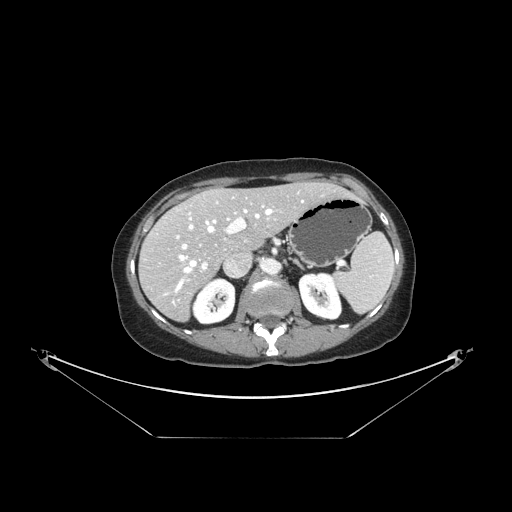
Contrast-enhanced abdominal CT, one axial slice. Slice 91 of 148 in the series (ordered by position). Intravenous contrast given. Soft-tissue window (W 400 / L 40 HU). 2.5 mm slice thickness. 512 × 512 image matrix. Female patient, age 73 years. Case-level facts recorded for this patient, not image findings: diagnosis: colorectal cancer liver metastases, imaged before liver resection; multiple liver metastases: no; largest metastasis: 1 cm; disease in both lobes: no.
Structures marked on this image (expert manual segmentation):
- hepatic veins: box from (x=176, y=201) to (x=303, y=291) px
- liver: (x=140, y=183)–(x=349, y=320)
- planned liver remnant (the part of the liver to remain after resection): (x=168, y=183)–(x=348, y=254)
- portal vein (with intrahepatic branches): (x=176, y=205)–(x=264, y=270)